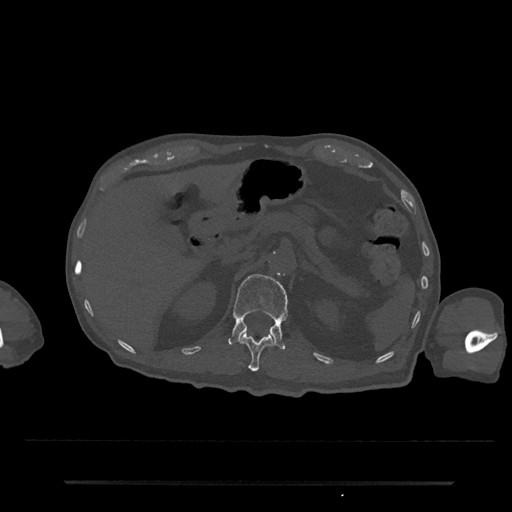
CT including the spine, one axial slice. Slice 159 of 797 in the series (ordered by position). Reconstruction kernel Br40s/3. Bone window (W 1800 / L 400 HU). 0.5 mm slice thickness. 512 × 512 image matrix, field of view 427 × 427 mm. Male patient, age 74 years. Case-level facts recorded for this patient, not image findings: primary cancer: prostate.
Annotated regions visible in this slice (semi-automatically segmented with operator editing):
- L1 vertebra: box from (x=228, y=274) to (x=288, y=350) px
- T12 vertebra: (x=240, y=333)–(x=273, y=372)